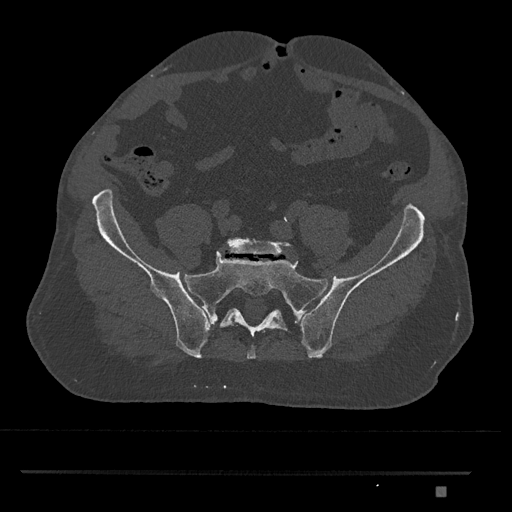
CT including the spine, one axial slice; position 501 of 1134 along the scan axis; reconstruction kernel Br40s/3; bone window (W 1800 / L 400 HU); 0.5 mm slice thickness; 512 × 512 image matrix, field of view 429 × 429 mm. Male patient, age 65 years. Case-level facts recorded for this patient, not image findings: primary cancer: prostate.
Annotated regions visible in this slice (semi-automatically segmented with operator editing):
- L5 vertebra: box from (x=225, y=237) to (x=294, y=257) px